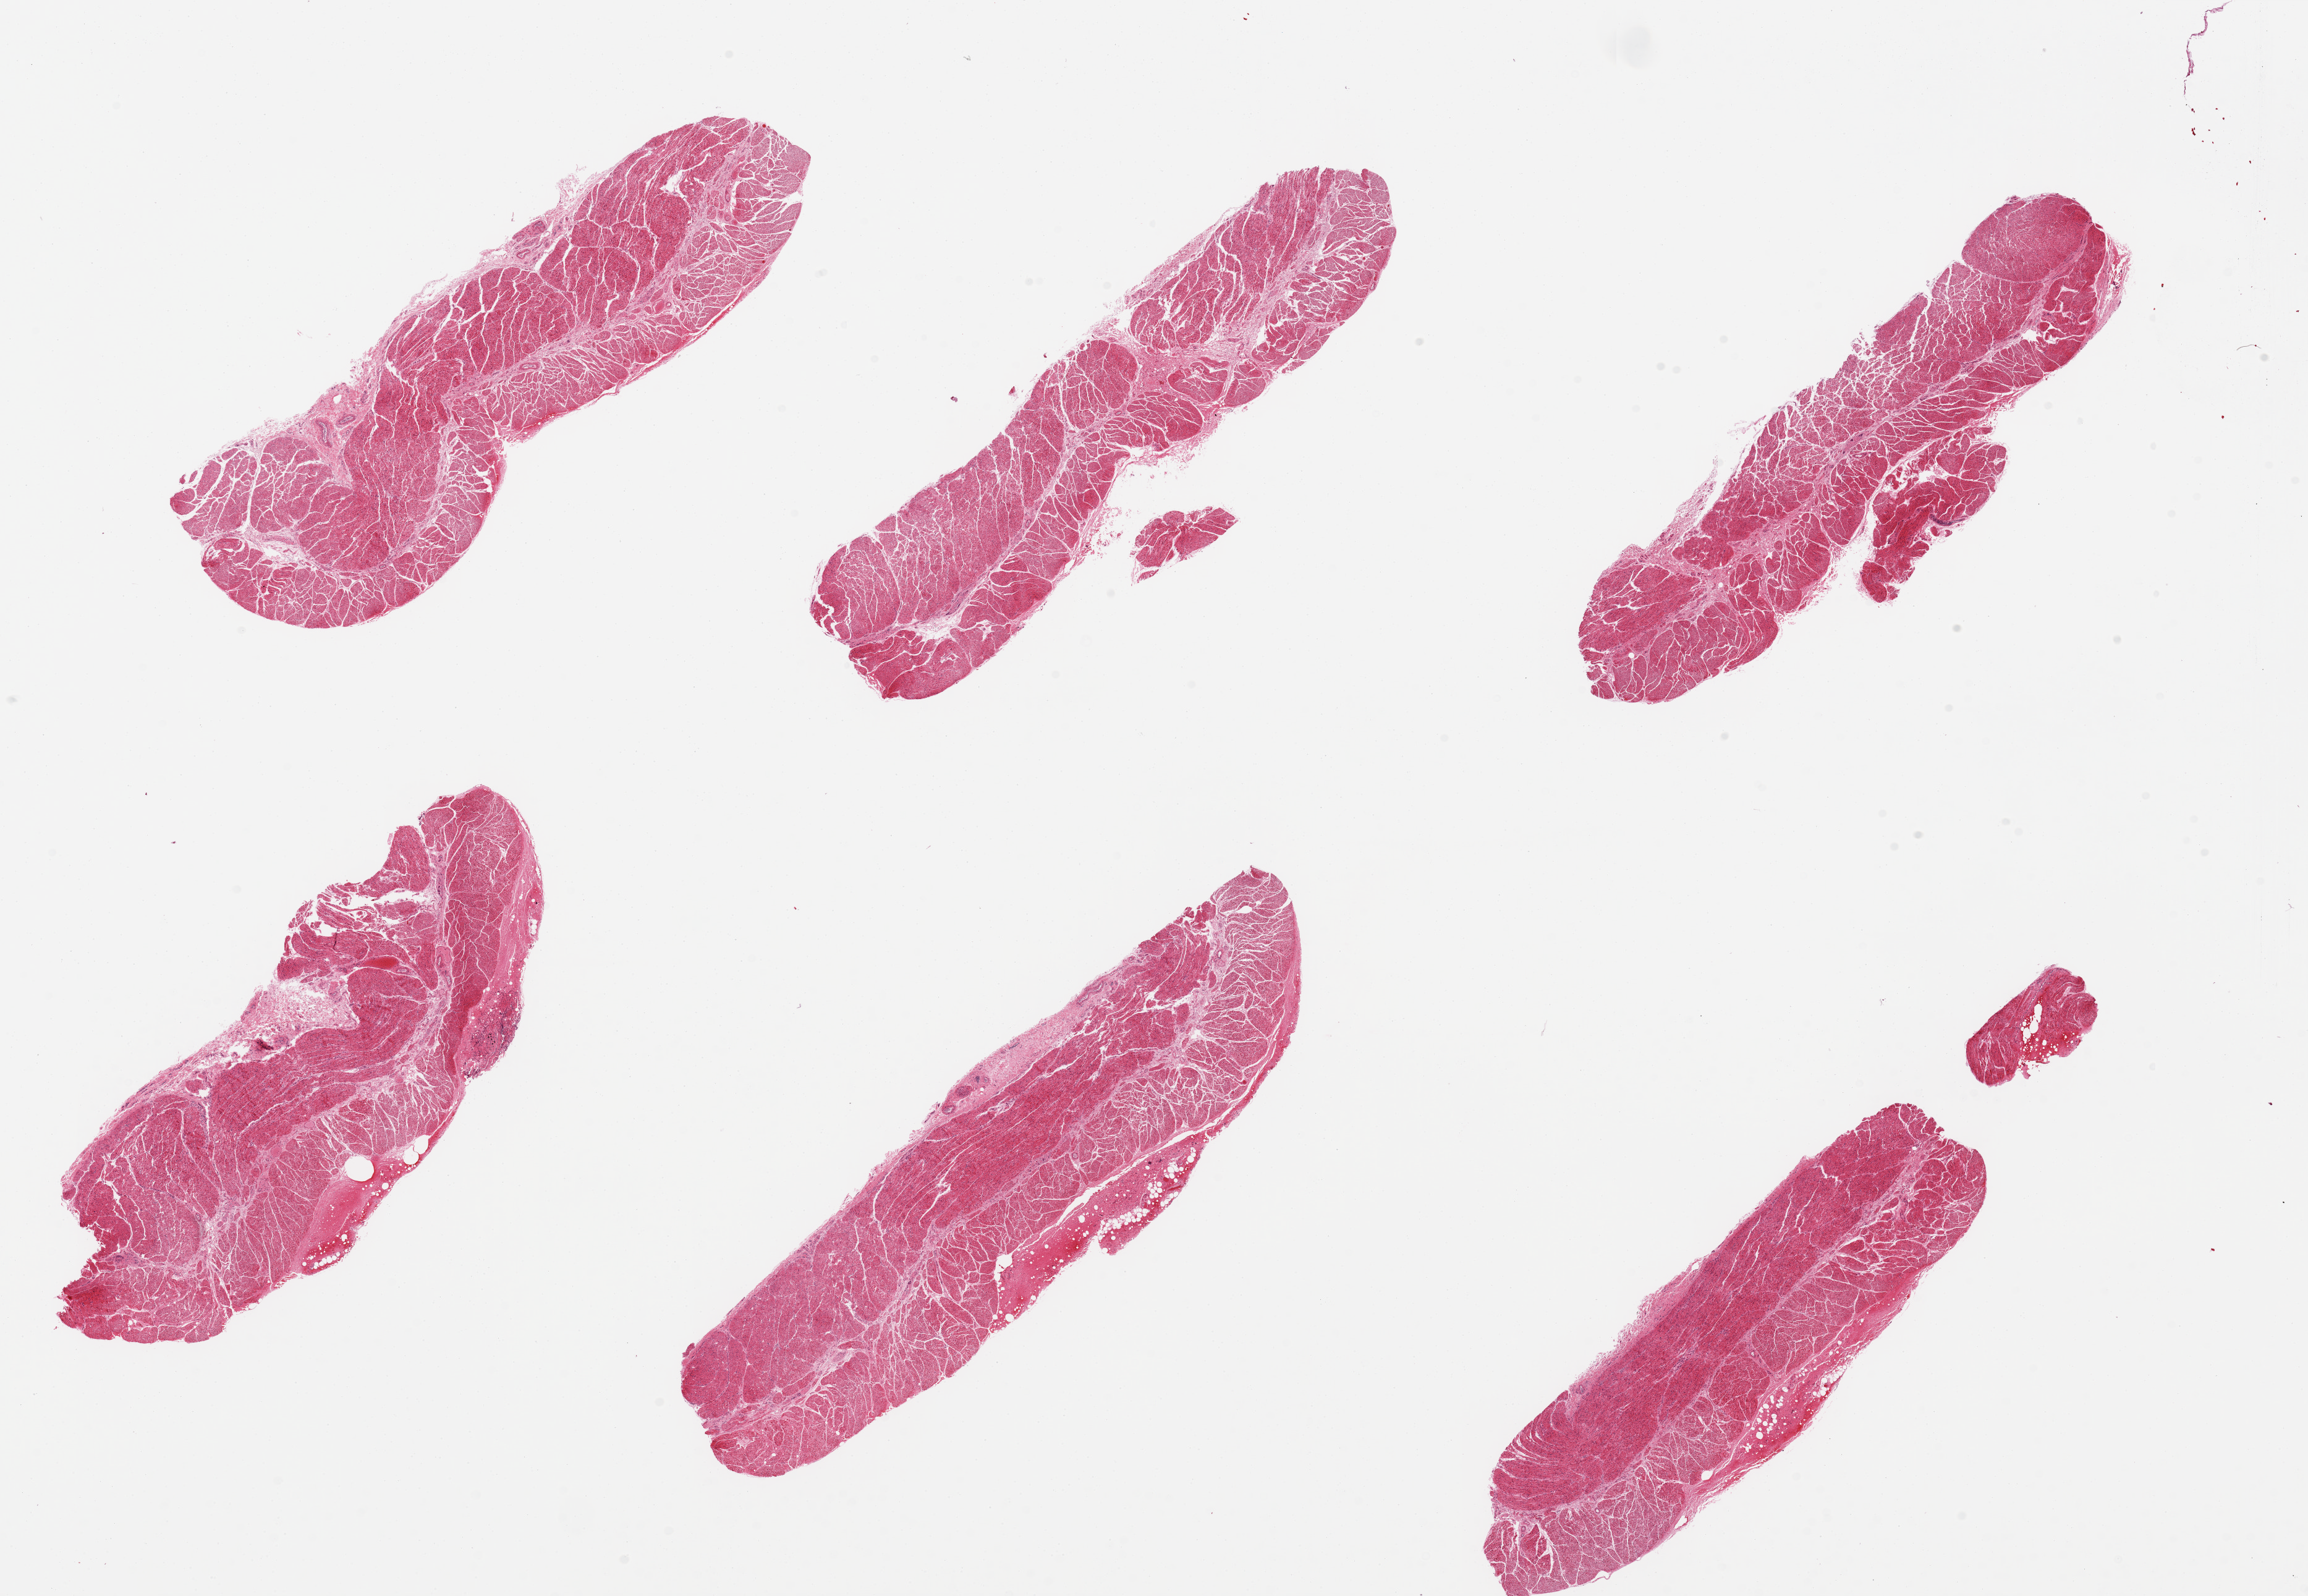
H&E whole-slide image, shown as a low-resolution overview of the whole scanned area (about 29.5 x 20.4 mm); PAXgene-fixed paraffin-embedded (PFPE) section; sampled site (target tissue): esophageal muscle; donor tissue sample. Donor: male.
Pathologist's review note for this sample: 6 pieces; well trimmed.